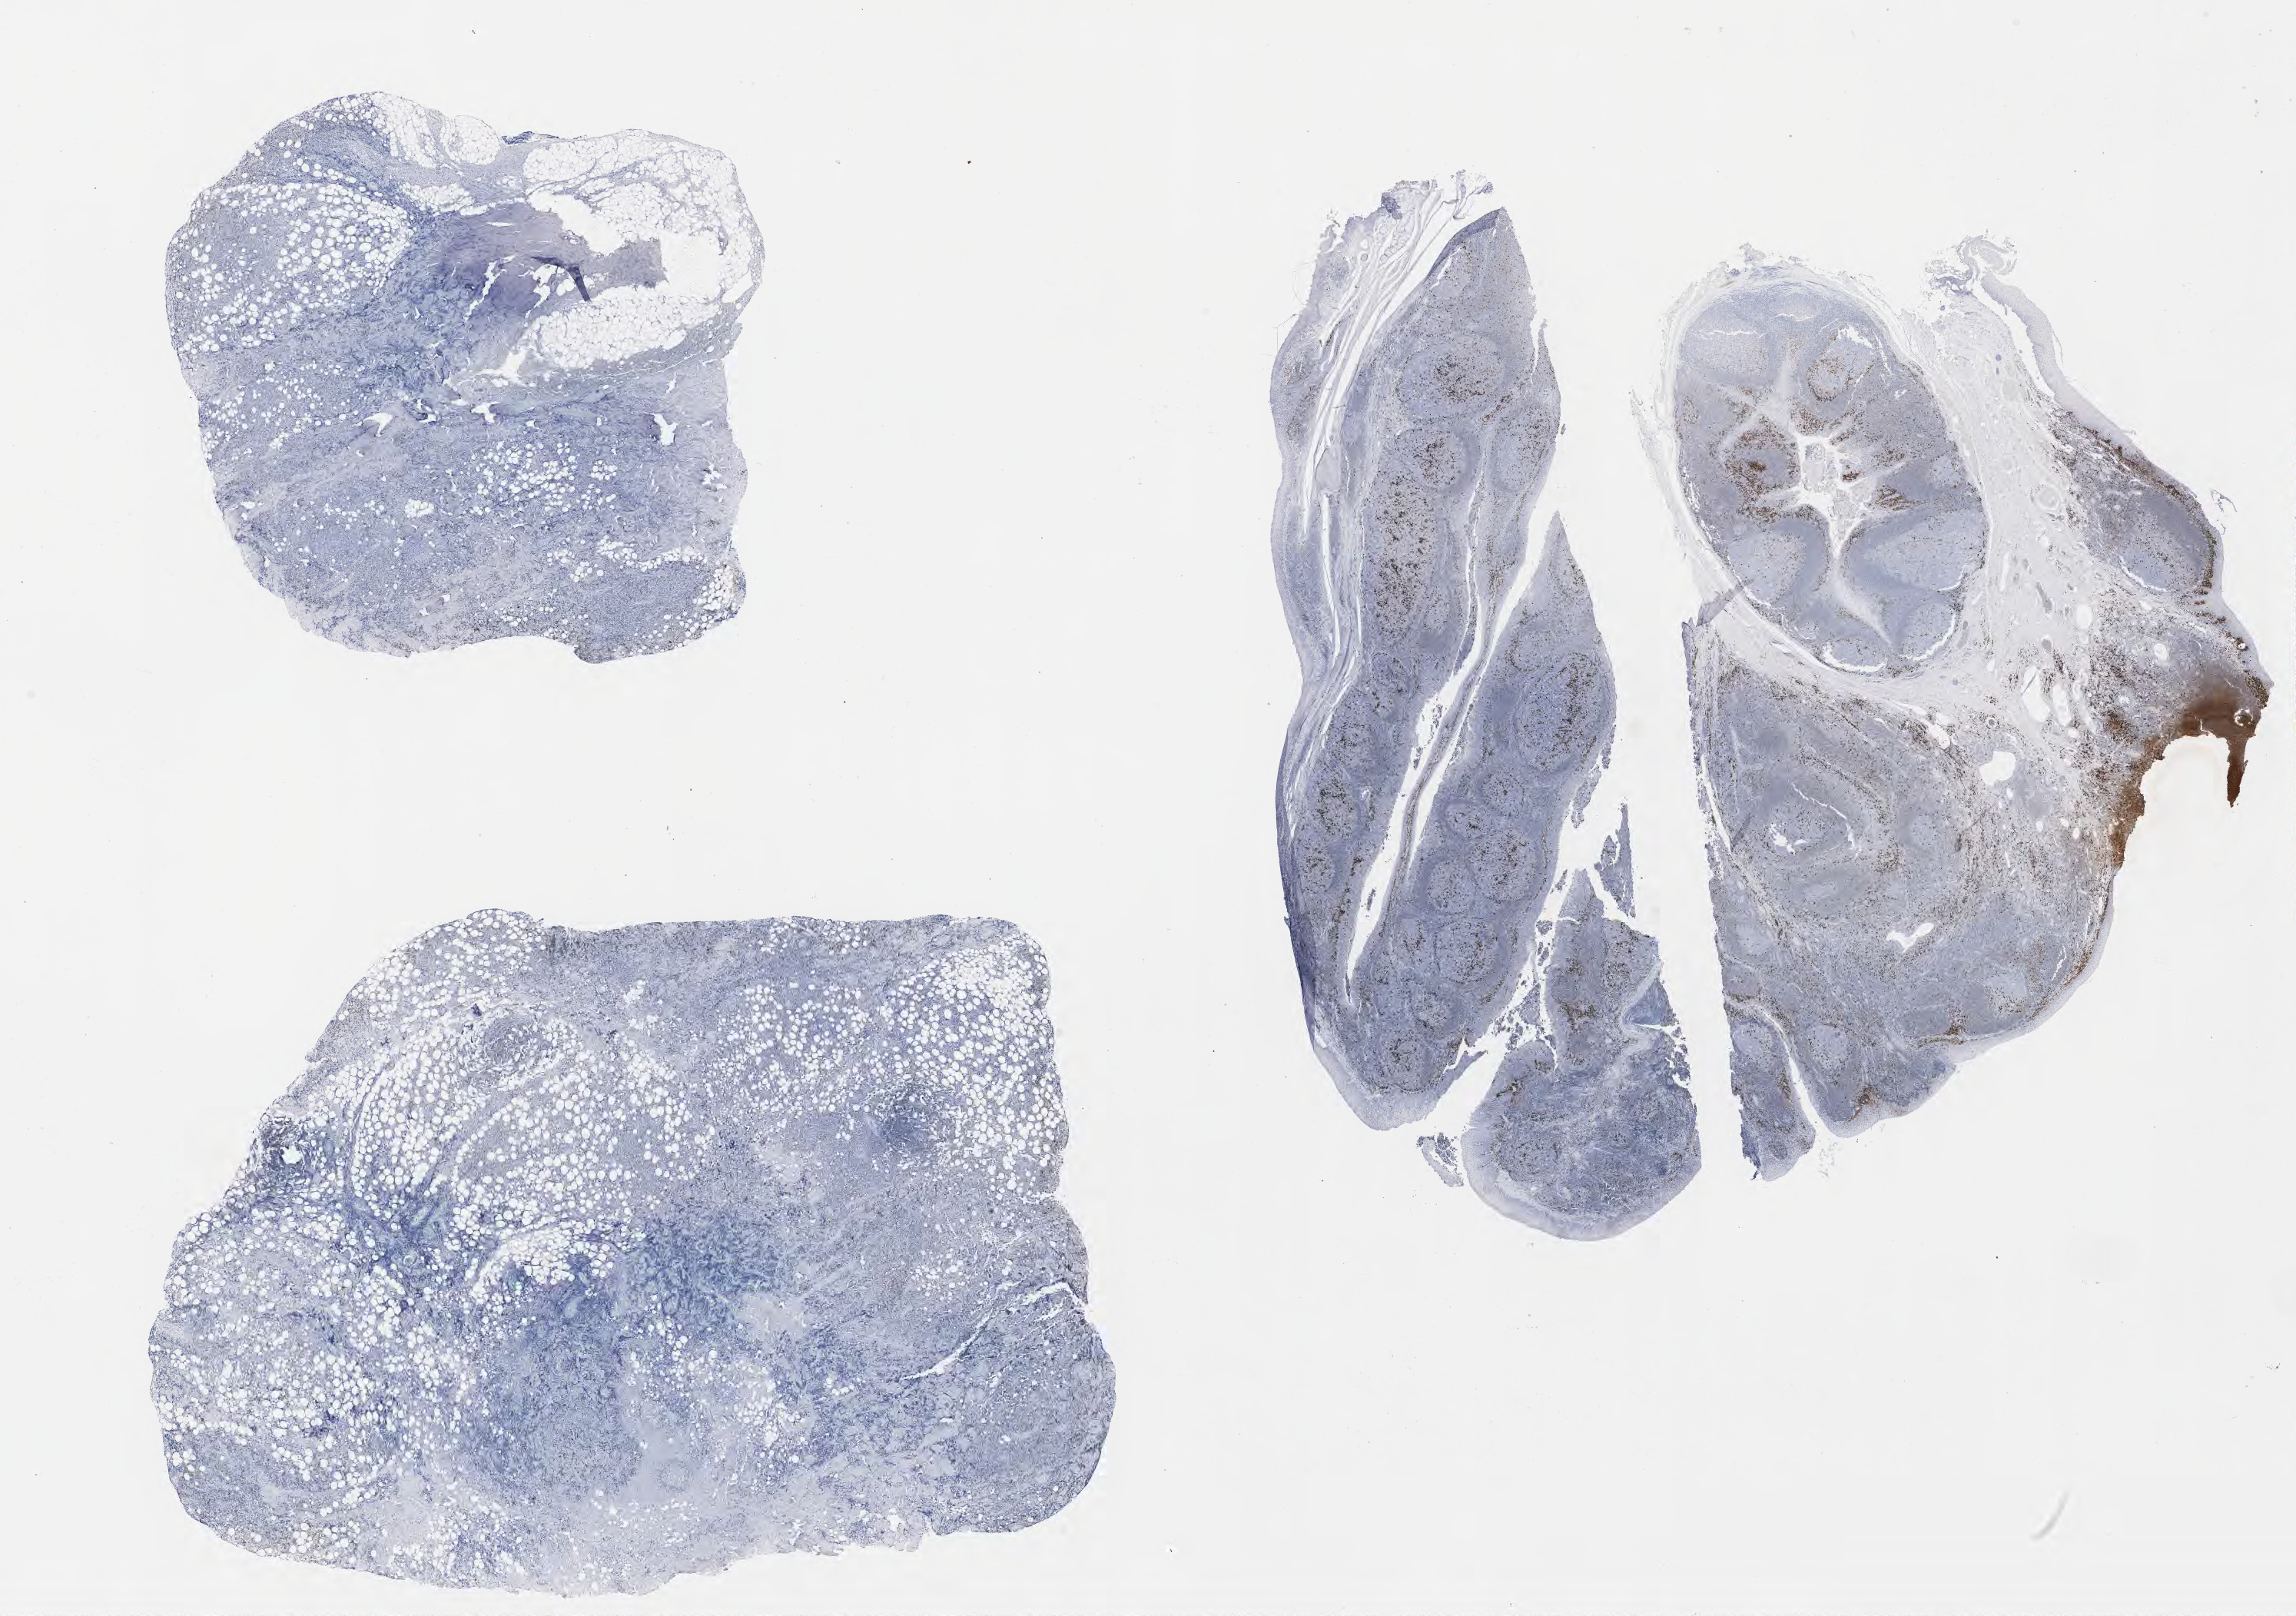
Immunohistochemistry (IHC) whole-slide image stained for IRF4/MUM1 — whole scanned area (about 24.1 x 17.0 mm) shown as a low-resolution overview. Tumor tissue. Anatomic site: kidney. Patient: male, aged 63.
Histologic diagnosis: Diffuse large B-cell lymphoma, NOS.